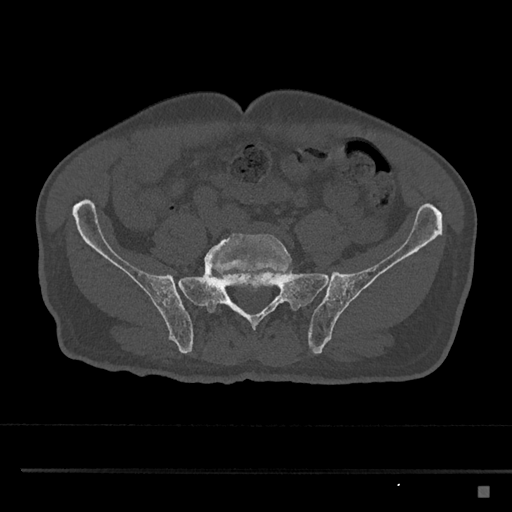
CT including the spine, one axial slice. Position 552 of 797 along the scan axis. Bone window (W 1800 / L 400 HU). 0.5 mm slice thickness. 512 × 512 image matrix. Patient: male, 59 years. From the clinical record (not read from this slice): primary cancer: prostate.
Annotated regions visible in this slice (semi-automatic segmentation, software-assisted and operator-edited):
- L5 vertebra: bounding box (x1, y1, x2, y2) in pixels: (204, 233, 294, 308)